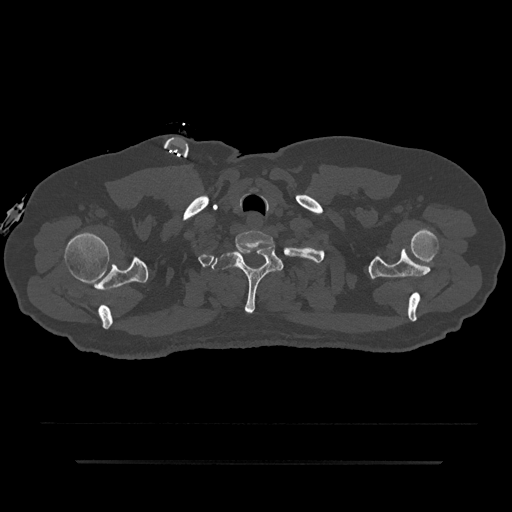
CT including the spine, one axial slice. Slice 743 of 797 in the series (ordered by position). Bone window (W 1800 / L 400 HU). 0.5 mm slice thickness. 512 × 512 image matrix. Male patient, age 59 years. Case-level facts recorded for this patient, not image findings: primary cancer: bile ducts.
Outlined on this slice (semi-automatically segmented with operator editing):
- T1 vertebra: bounding box <211,246,283,314> (left, top, right, bottom; pixels)